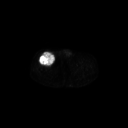
FDG PET of an extremity soft-tissue mass (from a PET/CT study), one axial slice. Position 290 of 311 along the scan axis. 3.27 mm slice thickness. 128 × 128 image matrix, field of view 700 × 700 mm. Patient: male, 56 years. From the clinical record (not read from this slice): histological type: pleiomorphic leiomyosarcoma; grade: intermediate; site of the primary tumour: right thigh.
Annotated regions visible in this slice (expert contour drawn on MRI and transferred to this co-registered scan by the dataset authors):
- gross tumour volume including surrounding oedema: bounding box (x1, y1, x2, y2) in pixels: (38, 52, 55, 66)
- gross tumour volume (mass): (39, 52, 55, 66)